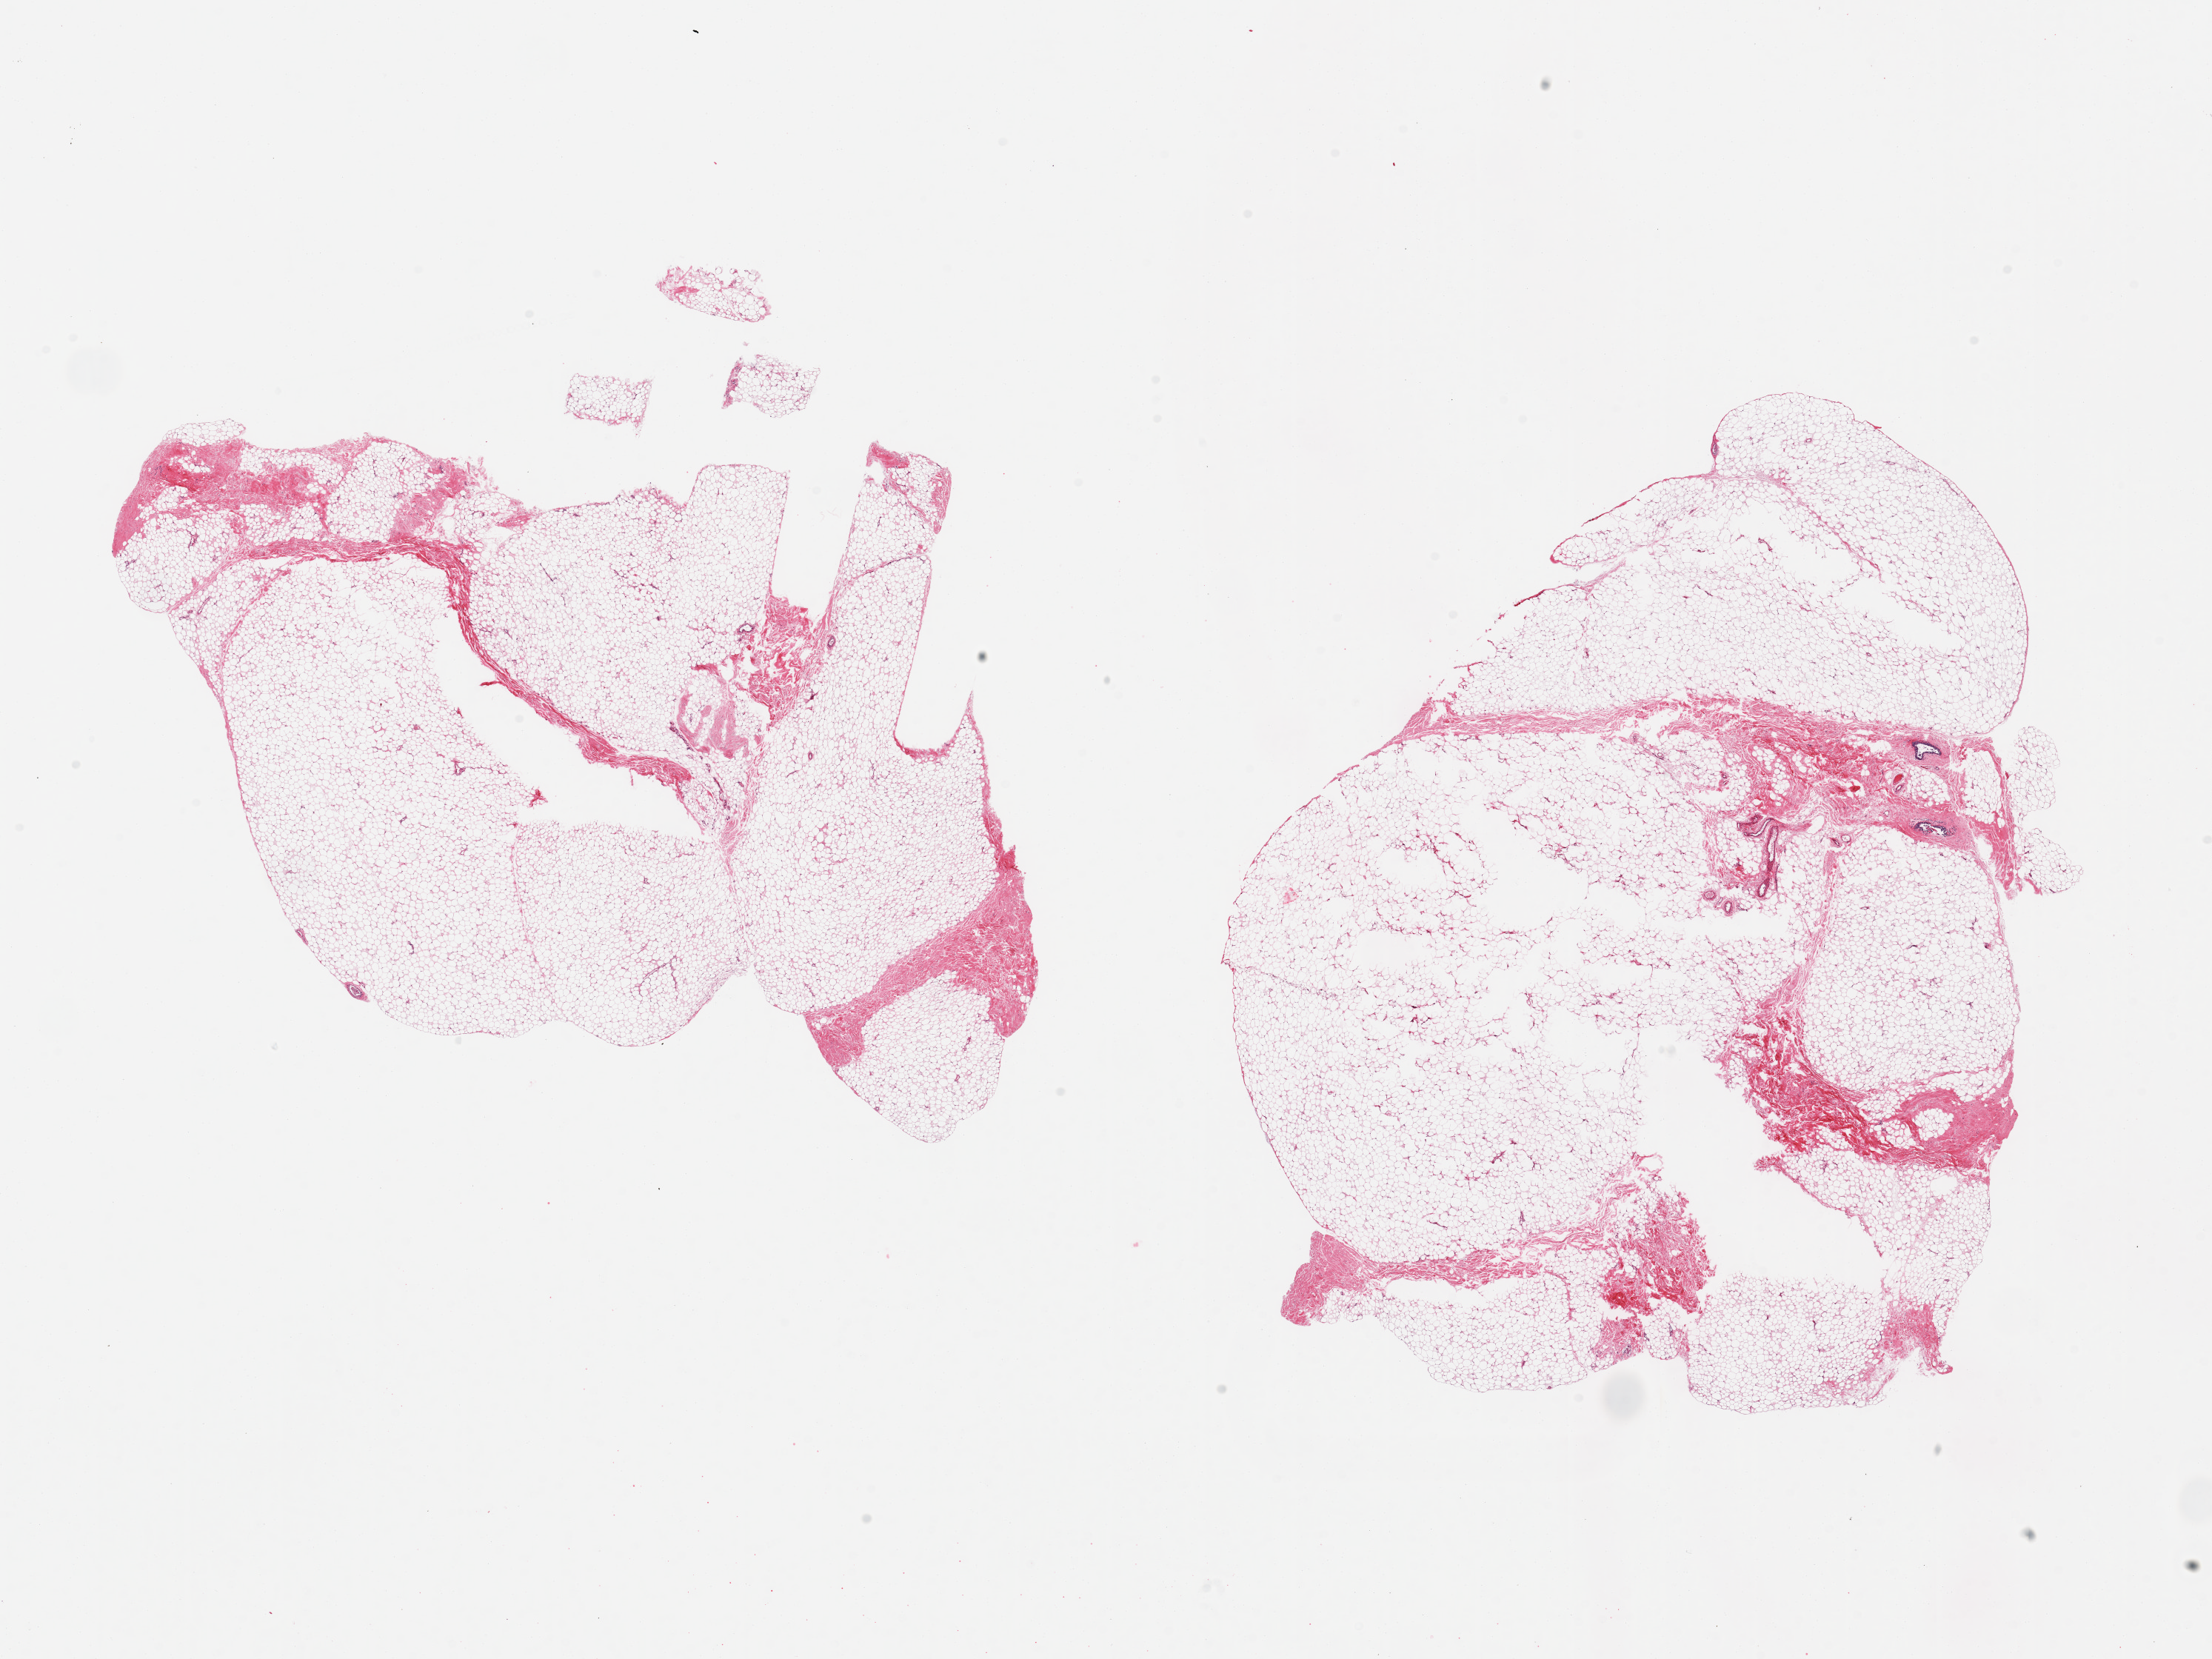
Haematoxylin and eosin whole-slide image — whole scanned area (about 23.6 x 17.7 mm) shown as a low-resolution overview; PAXgene-fixed paraffin-embedded (PFPE) section; sampled site (target tissue): breast; donor tissue sample.
Pathologist's review note for this sample: 2 pieces; mature adipose tissue with fibrovasular component and couple of ductal structures.